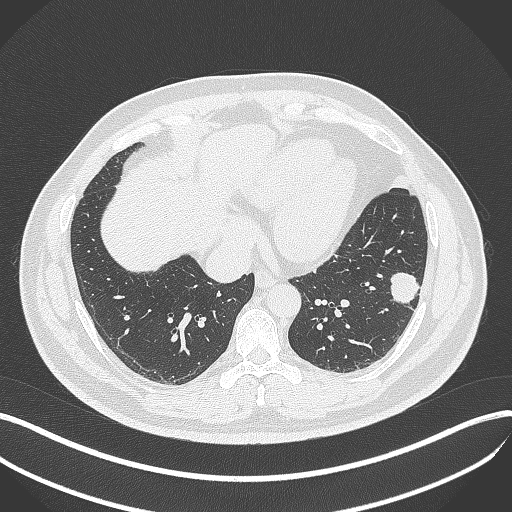
Chest CT, one axial slice. Reconstruction kernel B70f. 120 kVp. Lung window (W 1500 / L -600 HU). 1 mm slice thickness. 512 × 512 image matrix, field of view 400 × 400 mm. Male patient, age 39 years. From the clinical record (not read from this slice): clinical TNM (as recorded): T2a N0 M0.
Annotated regions visible in this slice (rectangle marked by the reading radiologist):
- lung tumour (recorded histology: adenocarcinoma): bounding box (x1, y1, x2, y2) in pixels: (386, 271, 421, 308)